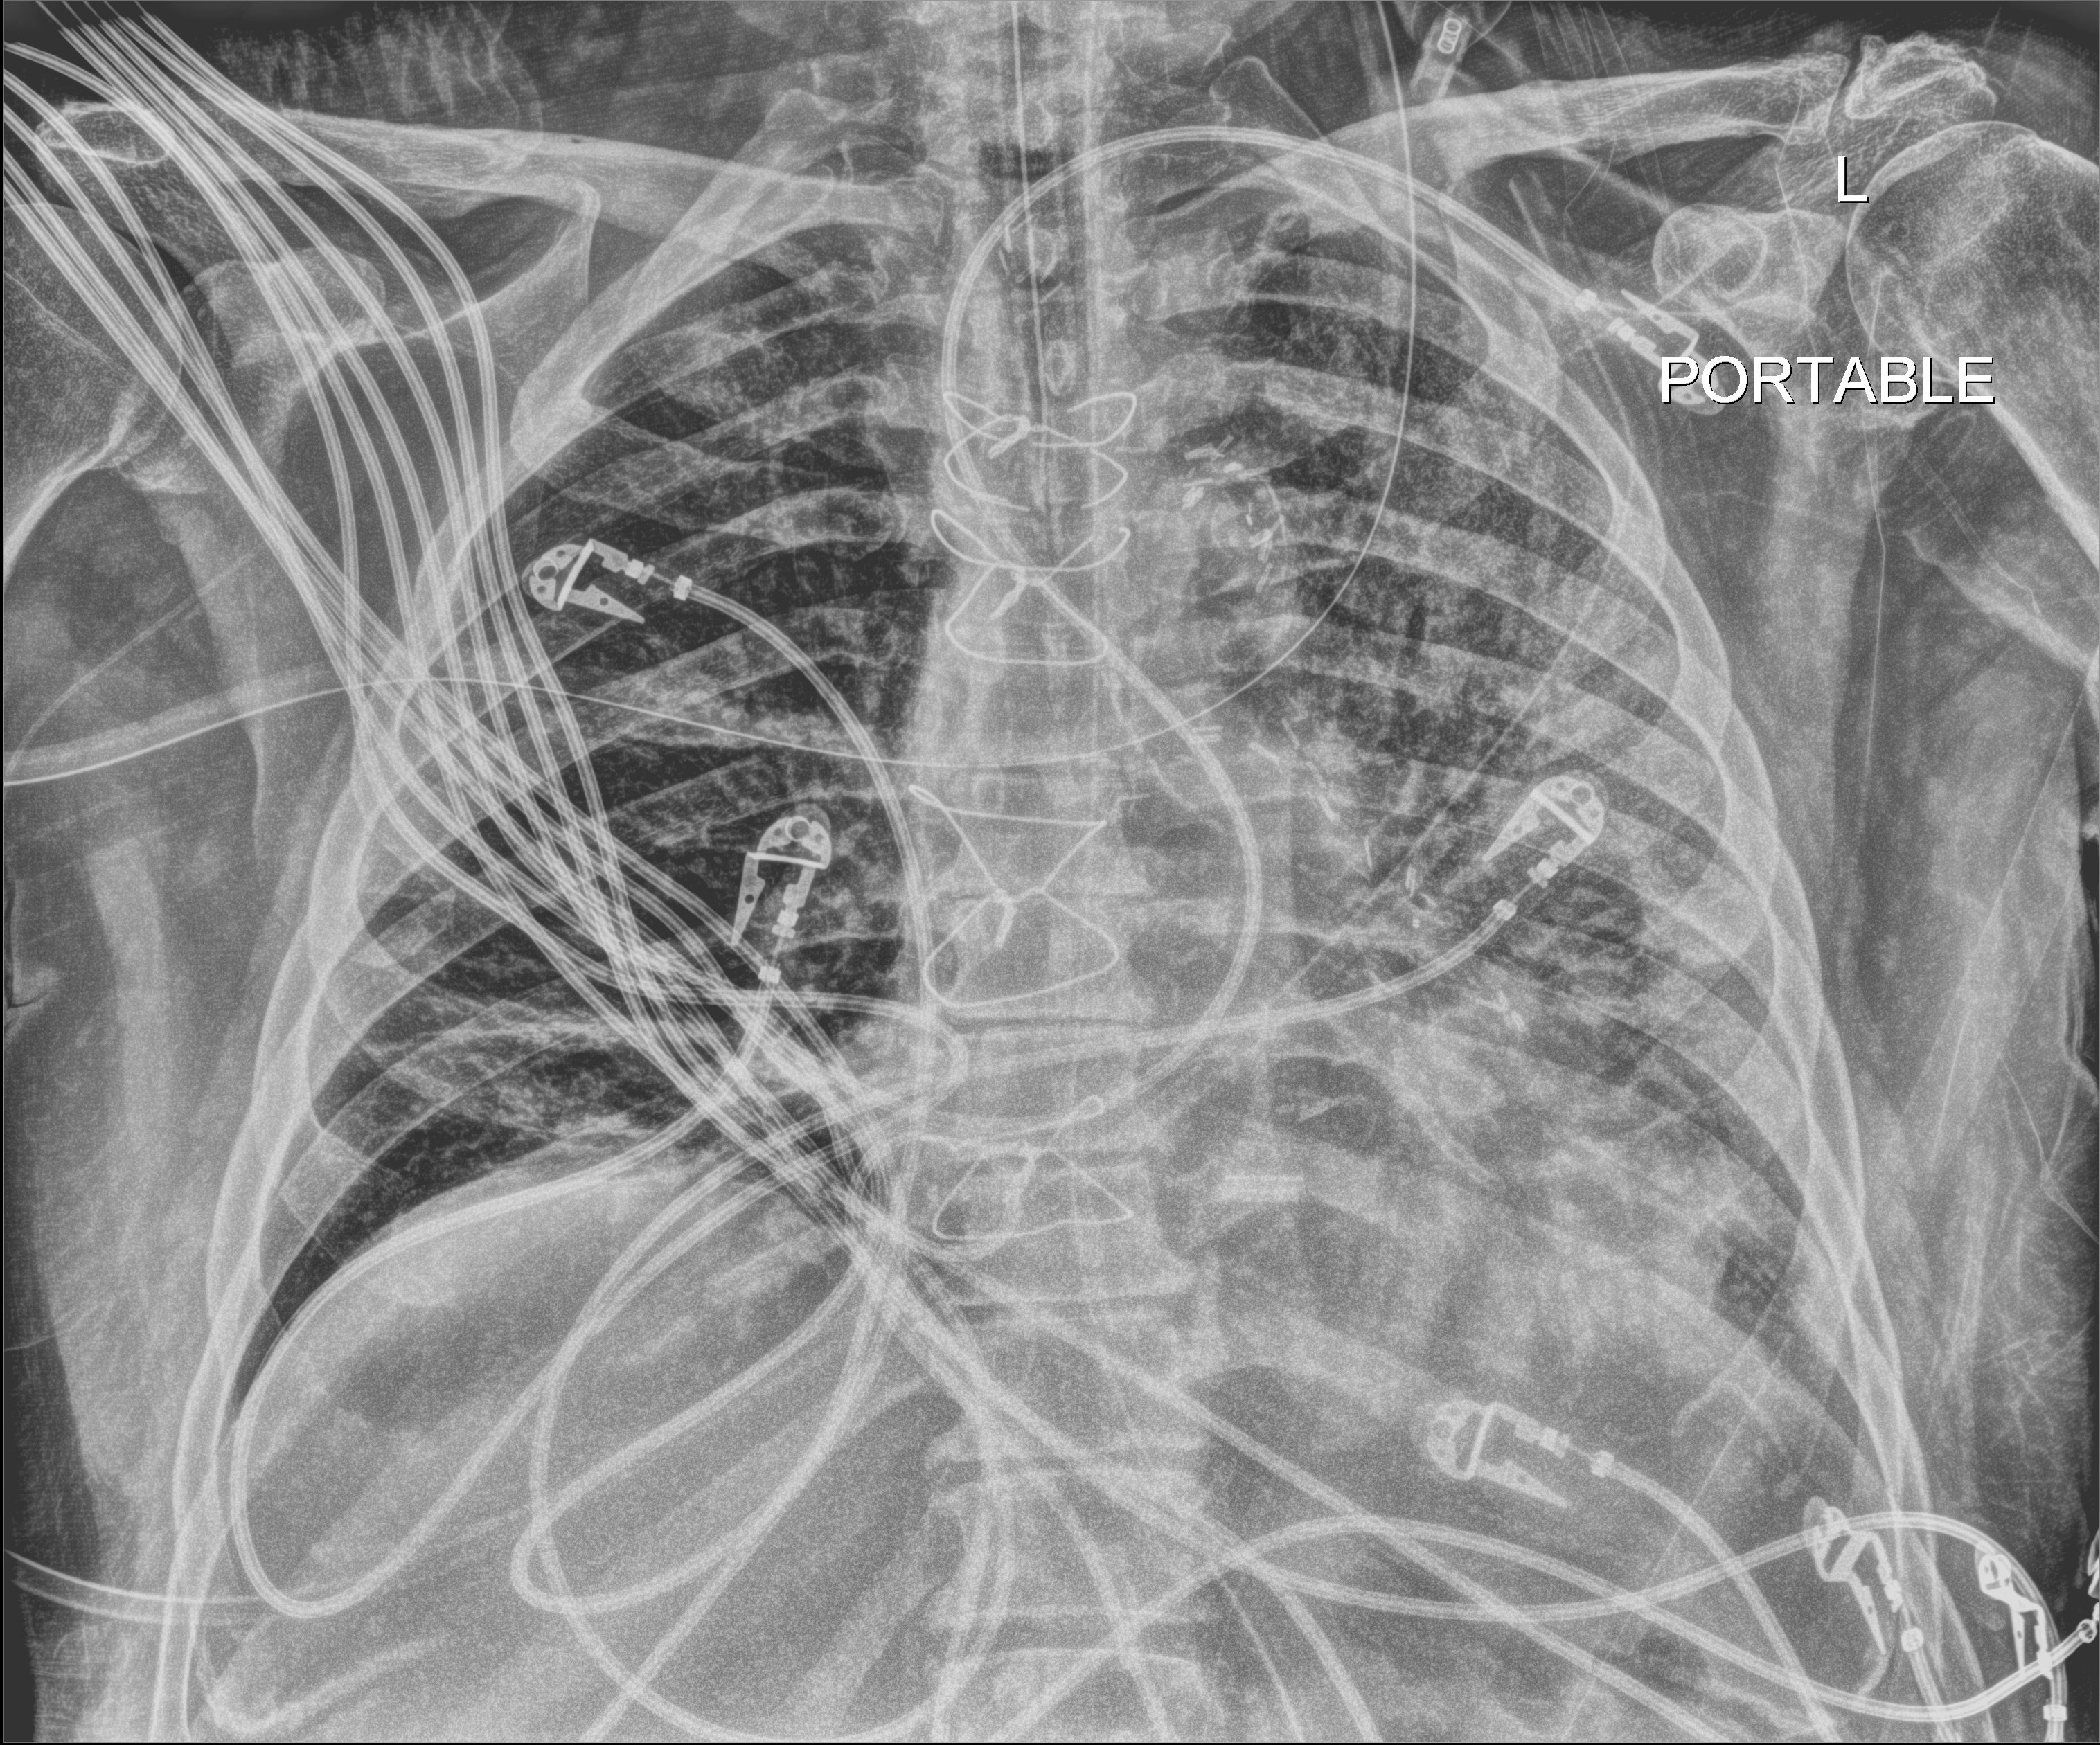
Chest X-ray (portable). Male patient hospitalised with COVID-19, age 60–74 years.
From the hospital-stay record, not from the radiograph (when in the stay this image was taken is not recorded): other chronic lung disease (admission record): no.